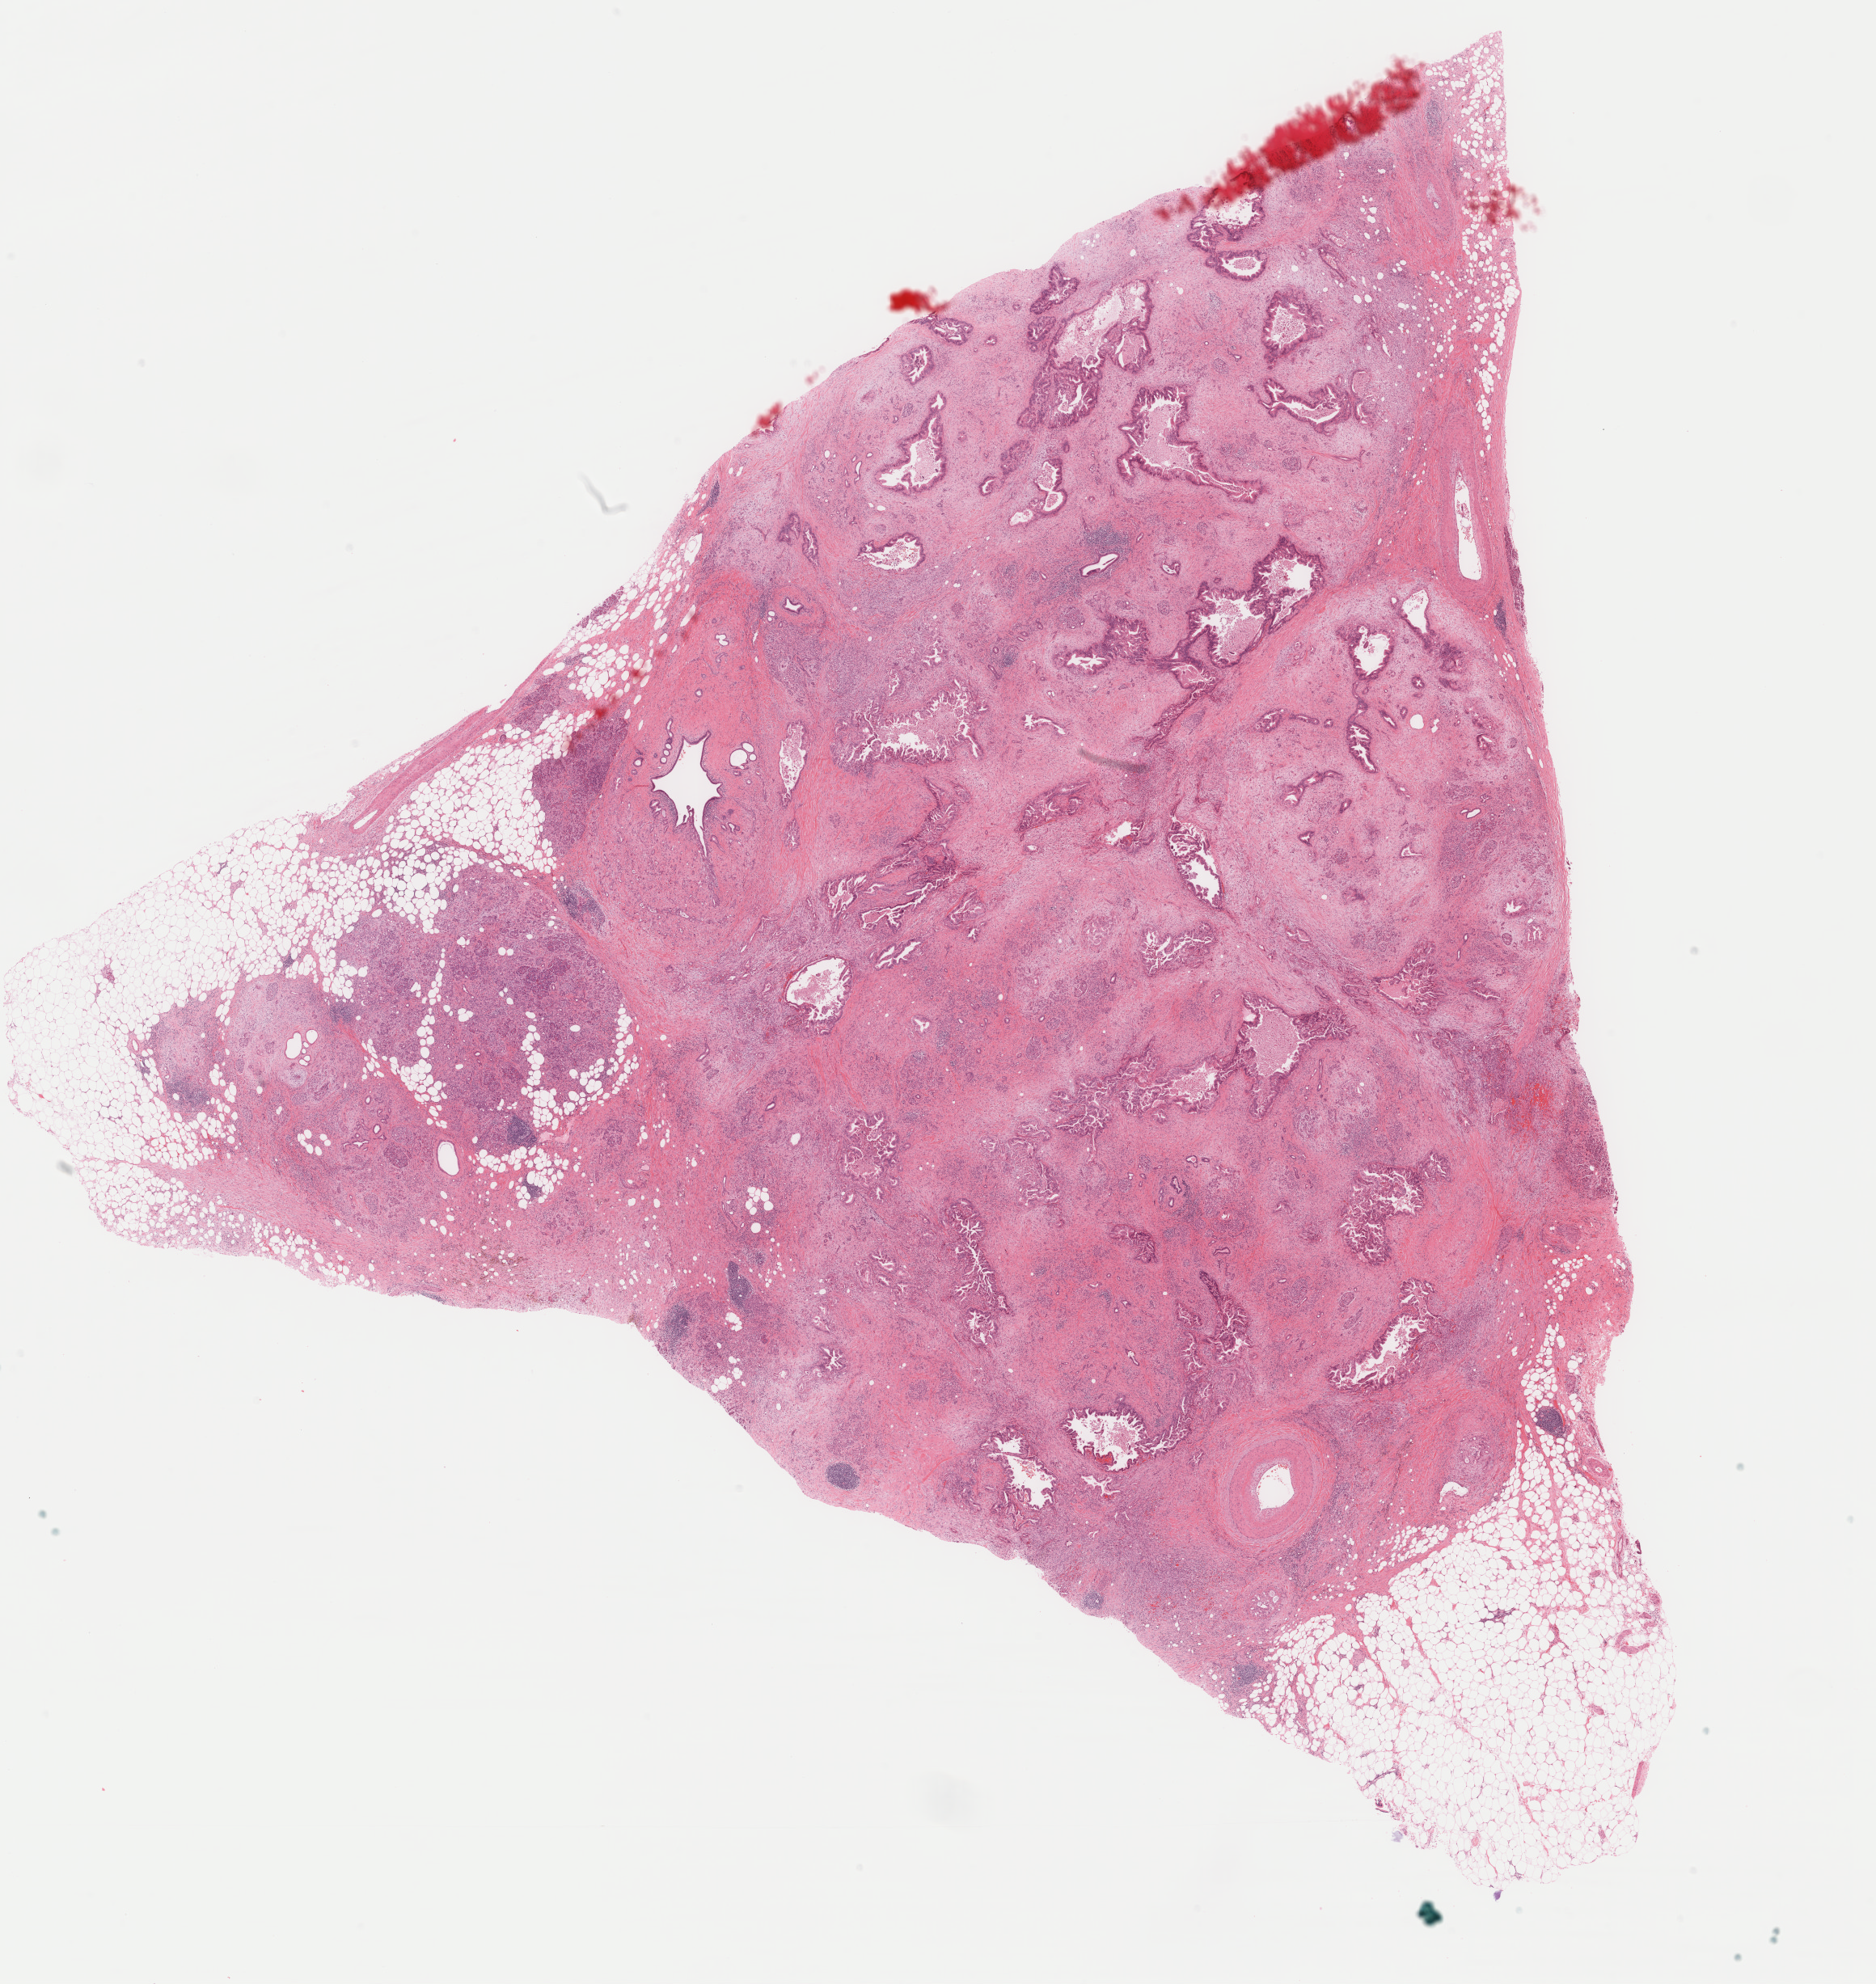
Hematoxylin and eosin (H&E) stained whole-slide image — whole scanned area (about 18.4 x 19.5 mm, from a 40x scan) shown as a low-resolution overview, formalin-fixed paraffin-embedded (FFPE) diagnostic section, pancreas, primary tumour sample. Patient: male, age at initial diagnosis 54 years. Histologic grade: G1 (well differentiated).
Histologic diagnosis: Infiltrating duct carcinoma, NOS. AJCC pathologic stage: IIB (7th edition).